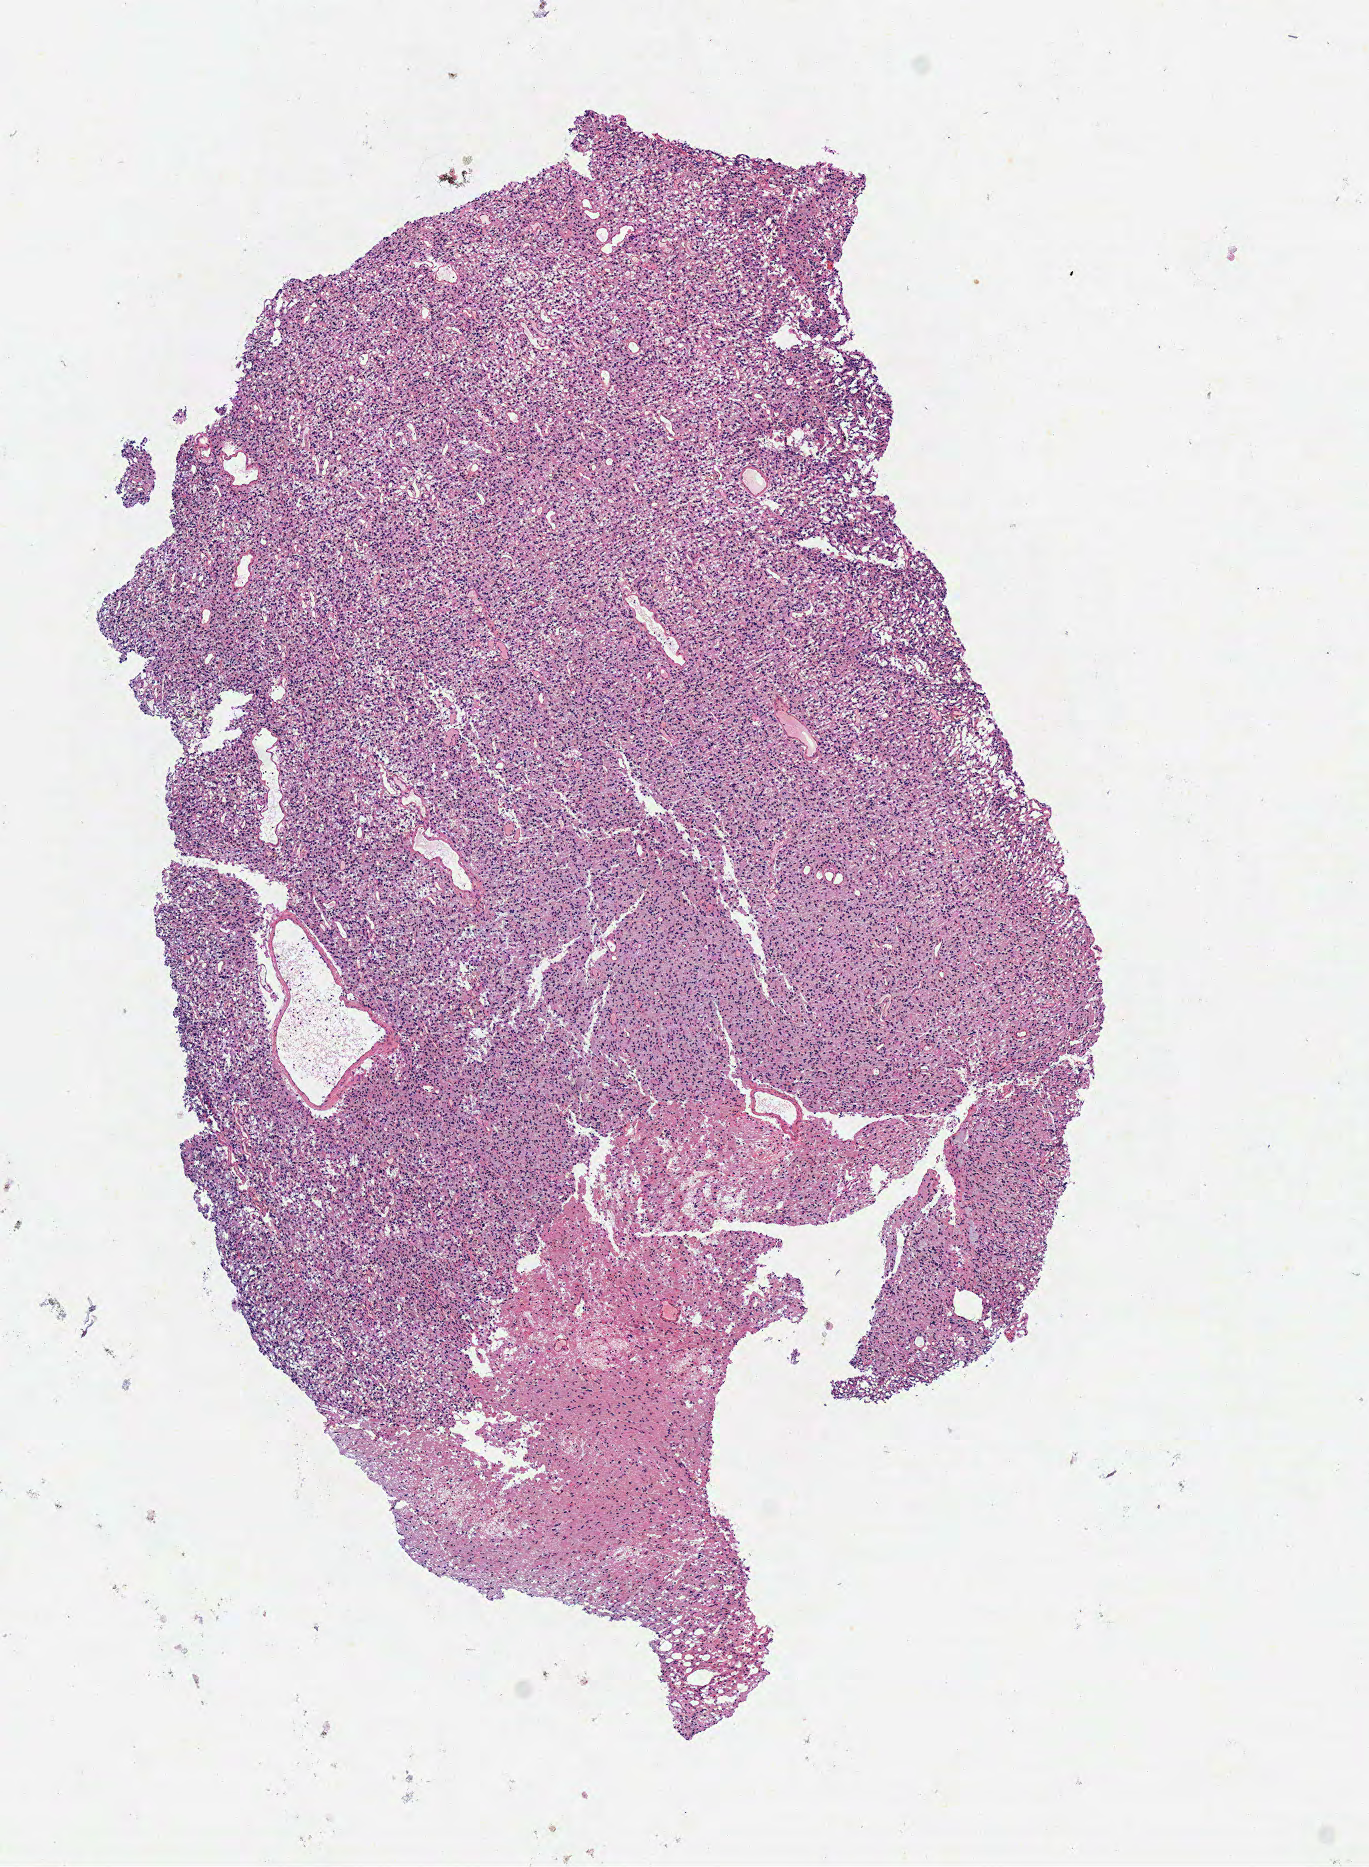
Hematoxylin and eosin (H&E) stained whole-slide image — shown as a low-resolution overview of the whole scanned area (about 5.4 x 7.3 mm, slide scanned at 40x). Frozen section from the top of the tissue portion. Sample: primary tumour, brain. Female, age 31 years at initial diagnosis. Slide review estimates, as recorded: tumour cells 100%, tumour nuclei 85%.
Pathologic diagnosis: Oligodendroglioma, NOS.